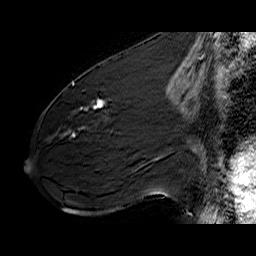
Breast MRI (dynamic contrast-enhanced), one sagittal slice. Position 31 of 60 along the scan axis. Dynamic contrast-enhanced series, time point 2 of 6 at this slice position (early post-contrast). 1.5 T. TE 6.4 ms, TR 32.9 ms. 4 mm slice thickness. 256 × 256 image matrix. Female patient. From the clinical record (not read from this slice): setting: breast cancer imaged before/during neoadjuvant chemotherapy; receptor status: HER2-positive.
Outlined on this slice (semi-automatic segmentation, software-assisted and operator-edited):
- analysis volume of interest (the breast-tissue region the enhancement analysis was run in; not a lesion): box from (x=61, y=77) to (x=141, y=142) px
- tumour enhancement mask (voxels above the 100 % enhancement threshold inside the analysis volume of interest): (x=73, y=82)–(x=104, y=129)